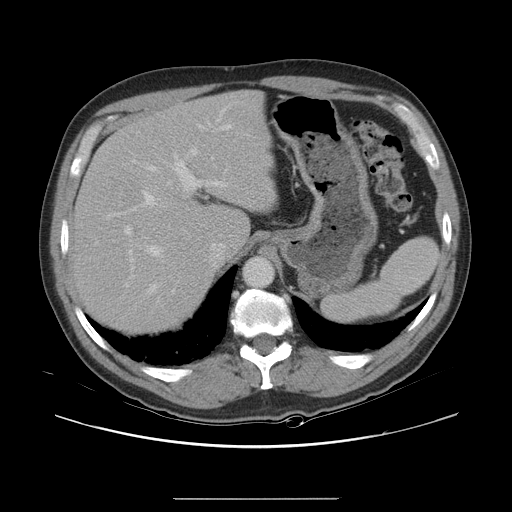
Contrast-enhanced abdominal CT, one axial slice; slice 21 of 40 in the series (ordered by position); 120 kVp; intravenous contrast given; soft-tissue window (W 400 / L 40 HU); 5 mm slice thickness; 512 × 512 image matrix. Male patient, age 64 years. Case-level facts recorded for this patient, not image findings: diagnosis: colorectal cancer liver metastases, imaged before liver resection; multiple liver metastases: yes; largest metastasis: 3.2 cm; disease in both lobes: yes.
Outlined on this slice (expert manual segmentation):
- hepatic veins: bounding box <110,191,161,293> (left, top, right, bottom; pixels)
- liver: <76,93,270,333>
- planned liver remnant (the part of the liver to remain after resection): <81,92,270,255>
- portal vein (with intrahepatic branches): <124,111,230,292>